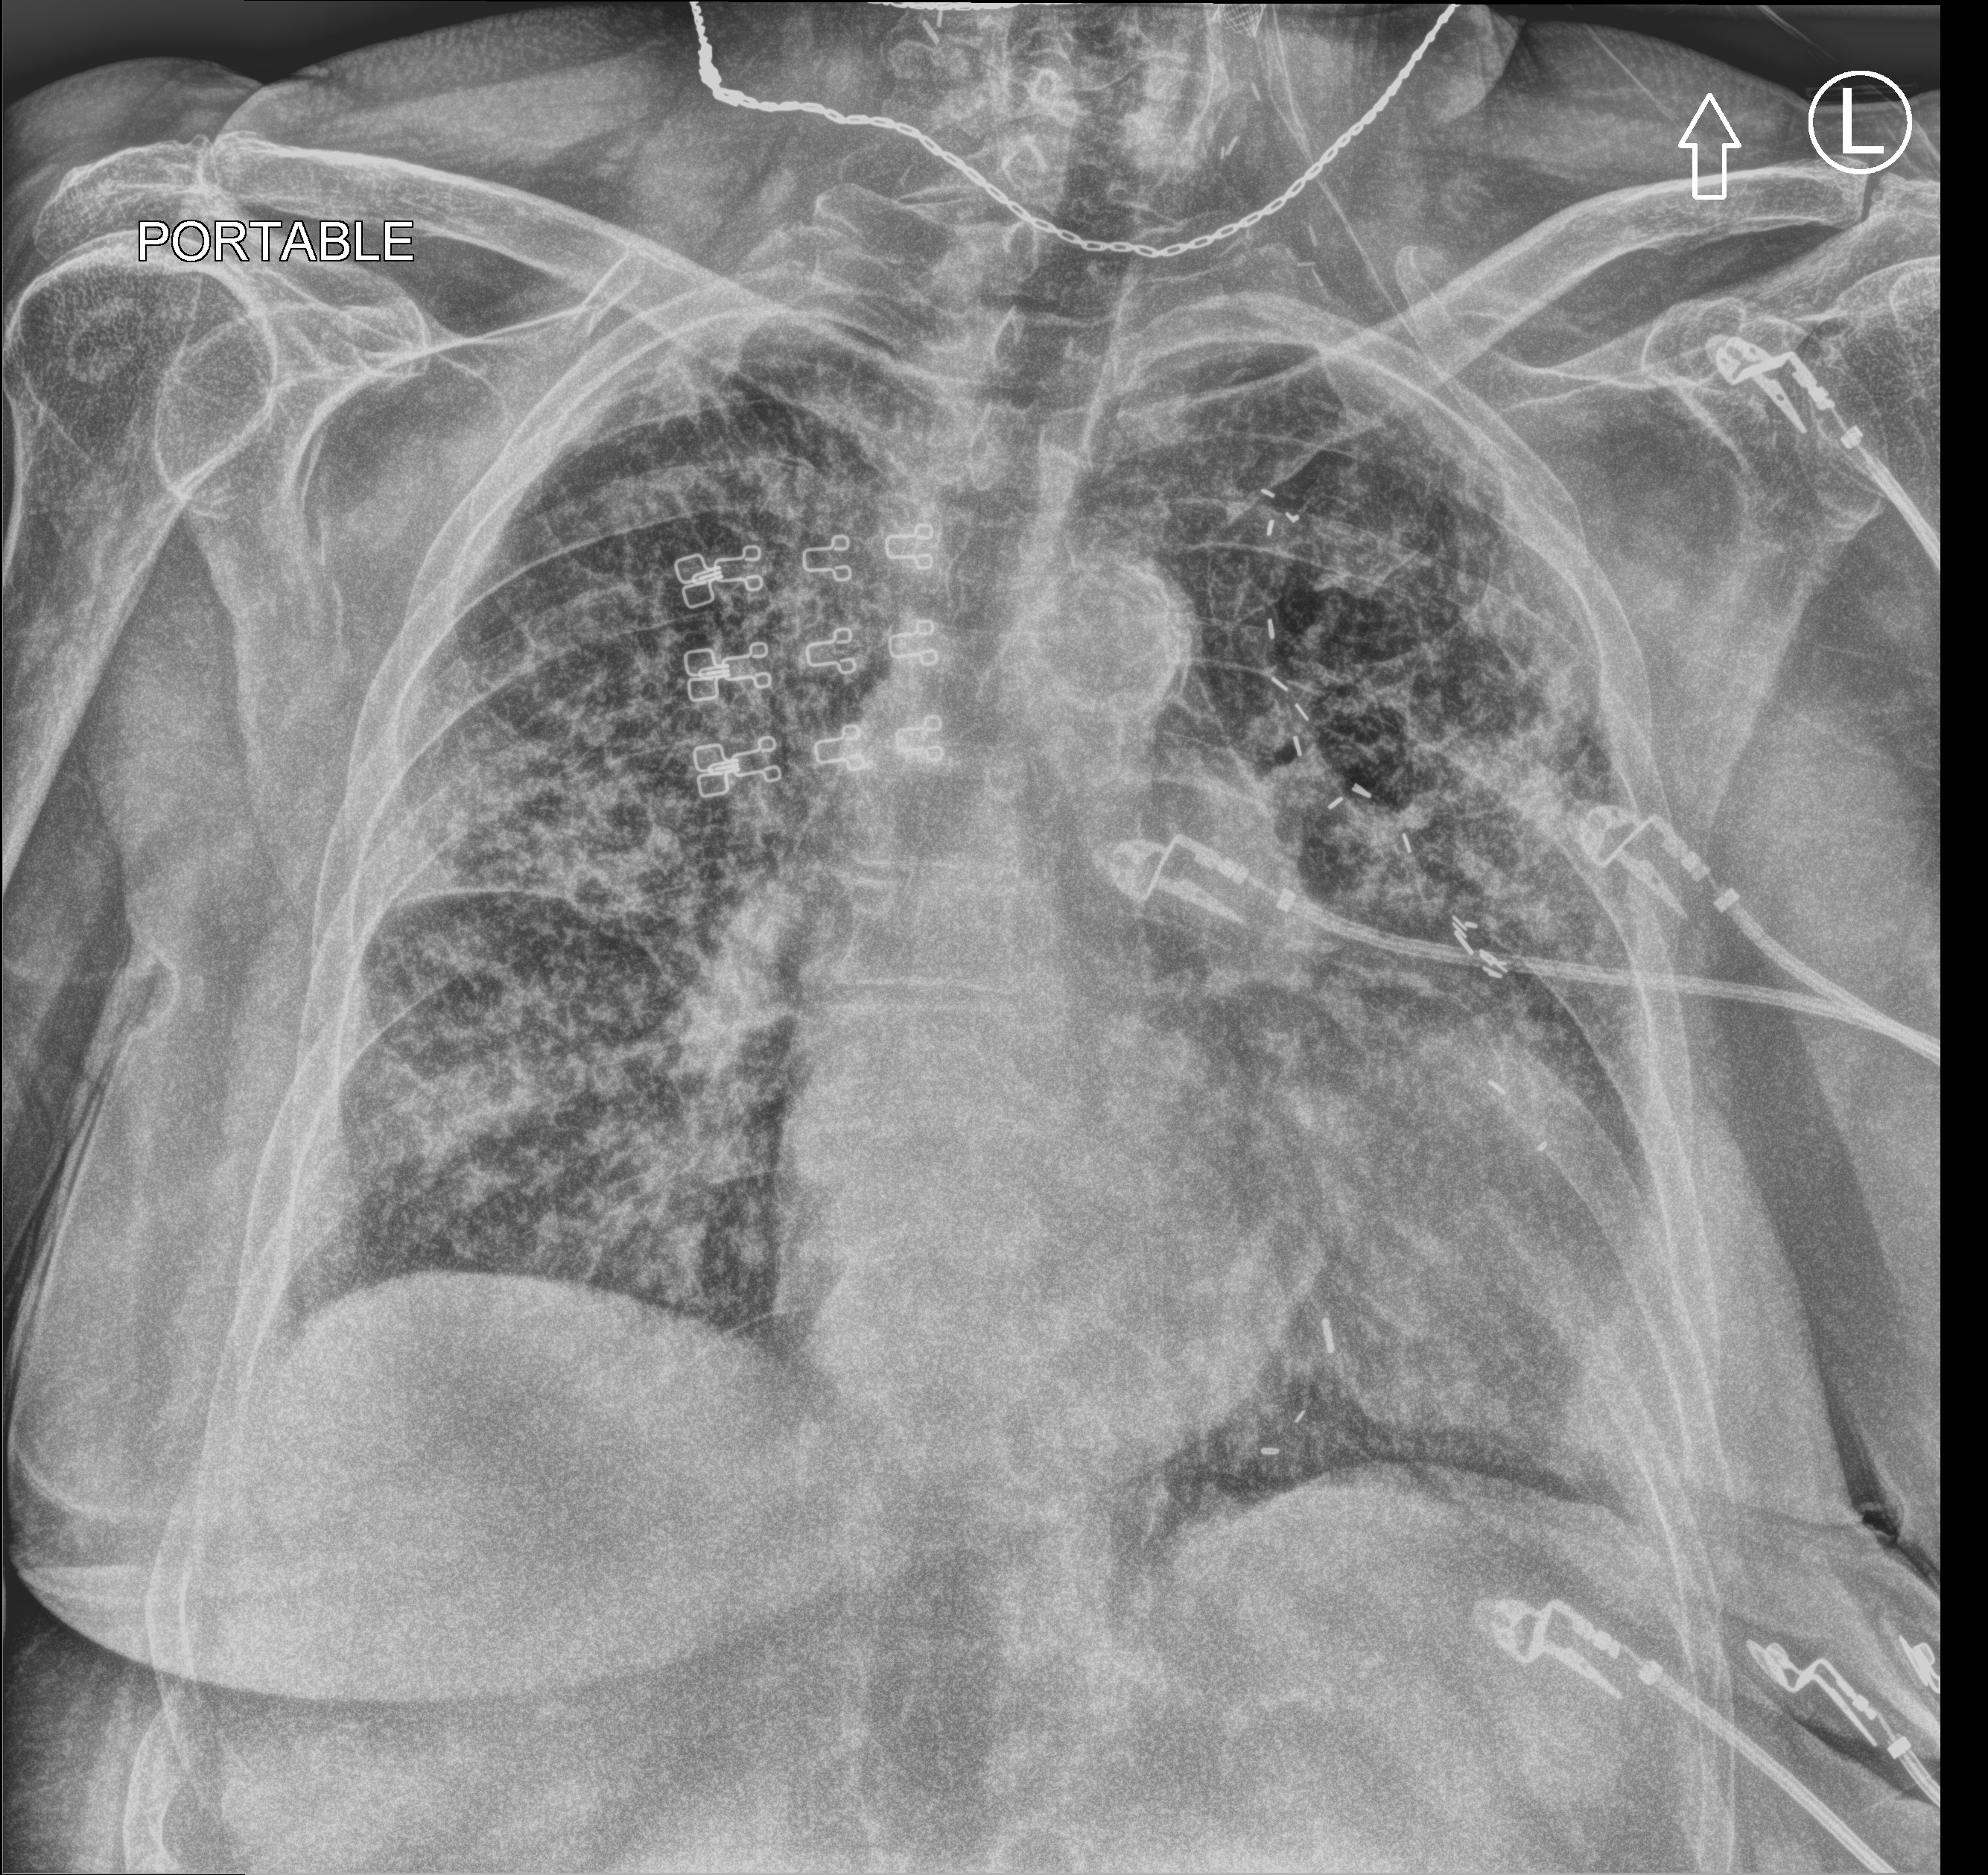
Chest X-ray (portable); anteroposterior (AP) projection. Female patient hospitalised with COVID-19, age 75–90 years.
From the hospital-stay record, not from the radiograph (when in the stay this image was taken is not recorded):
- admitted to intensive care during this hospital stay: no